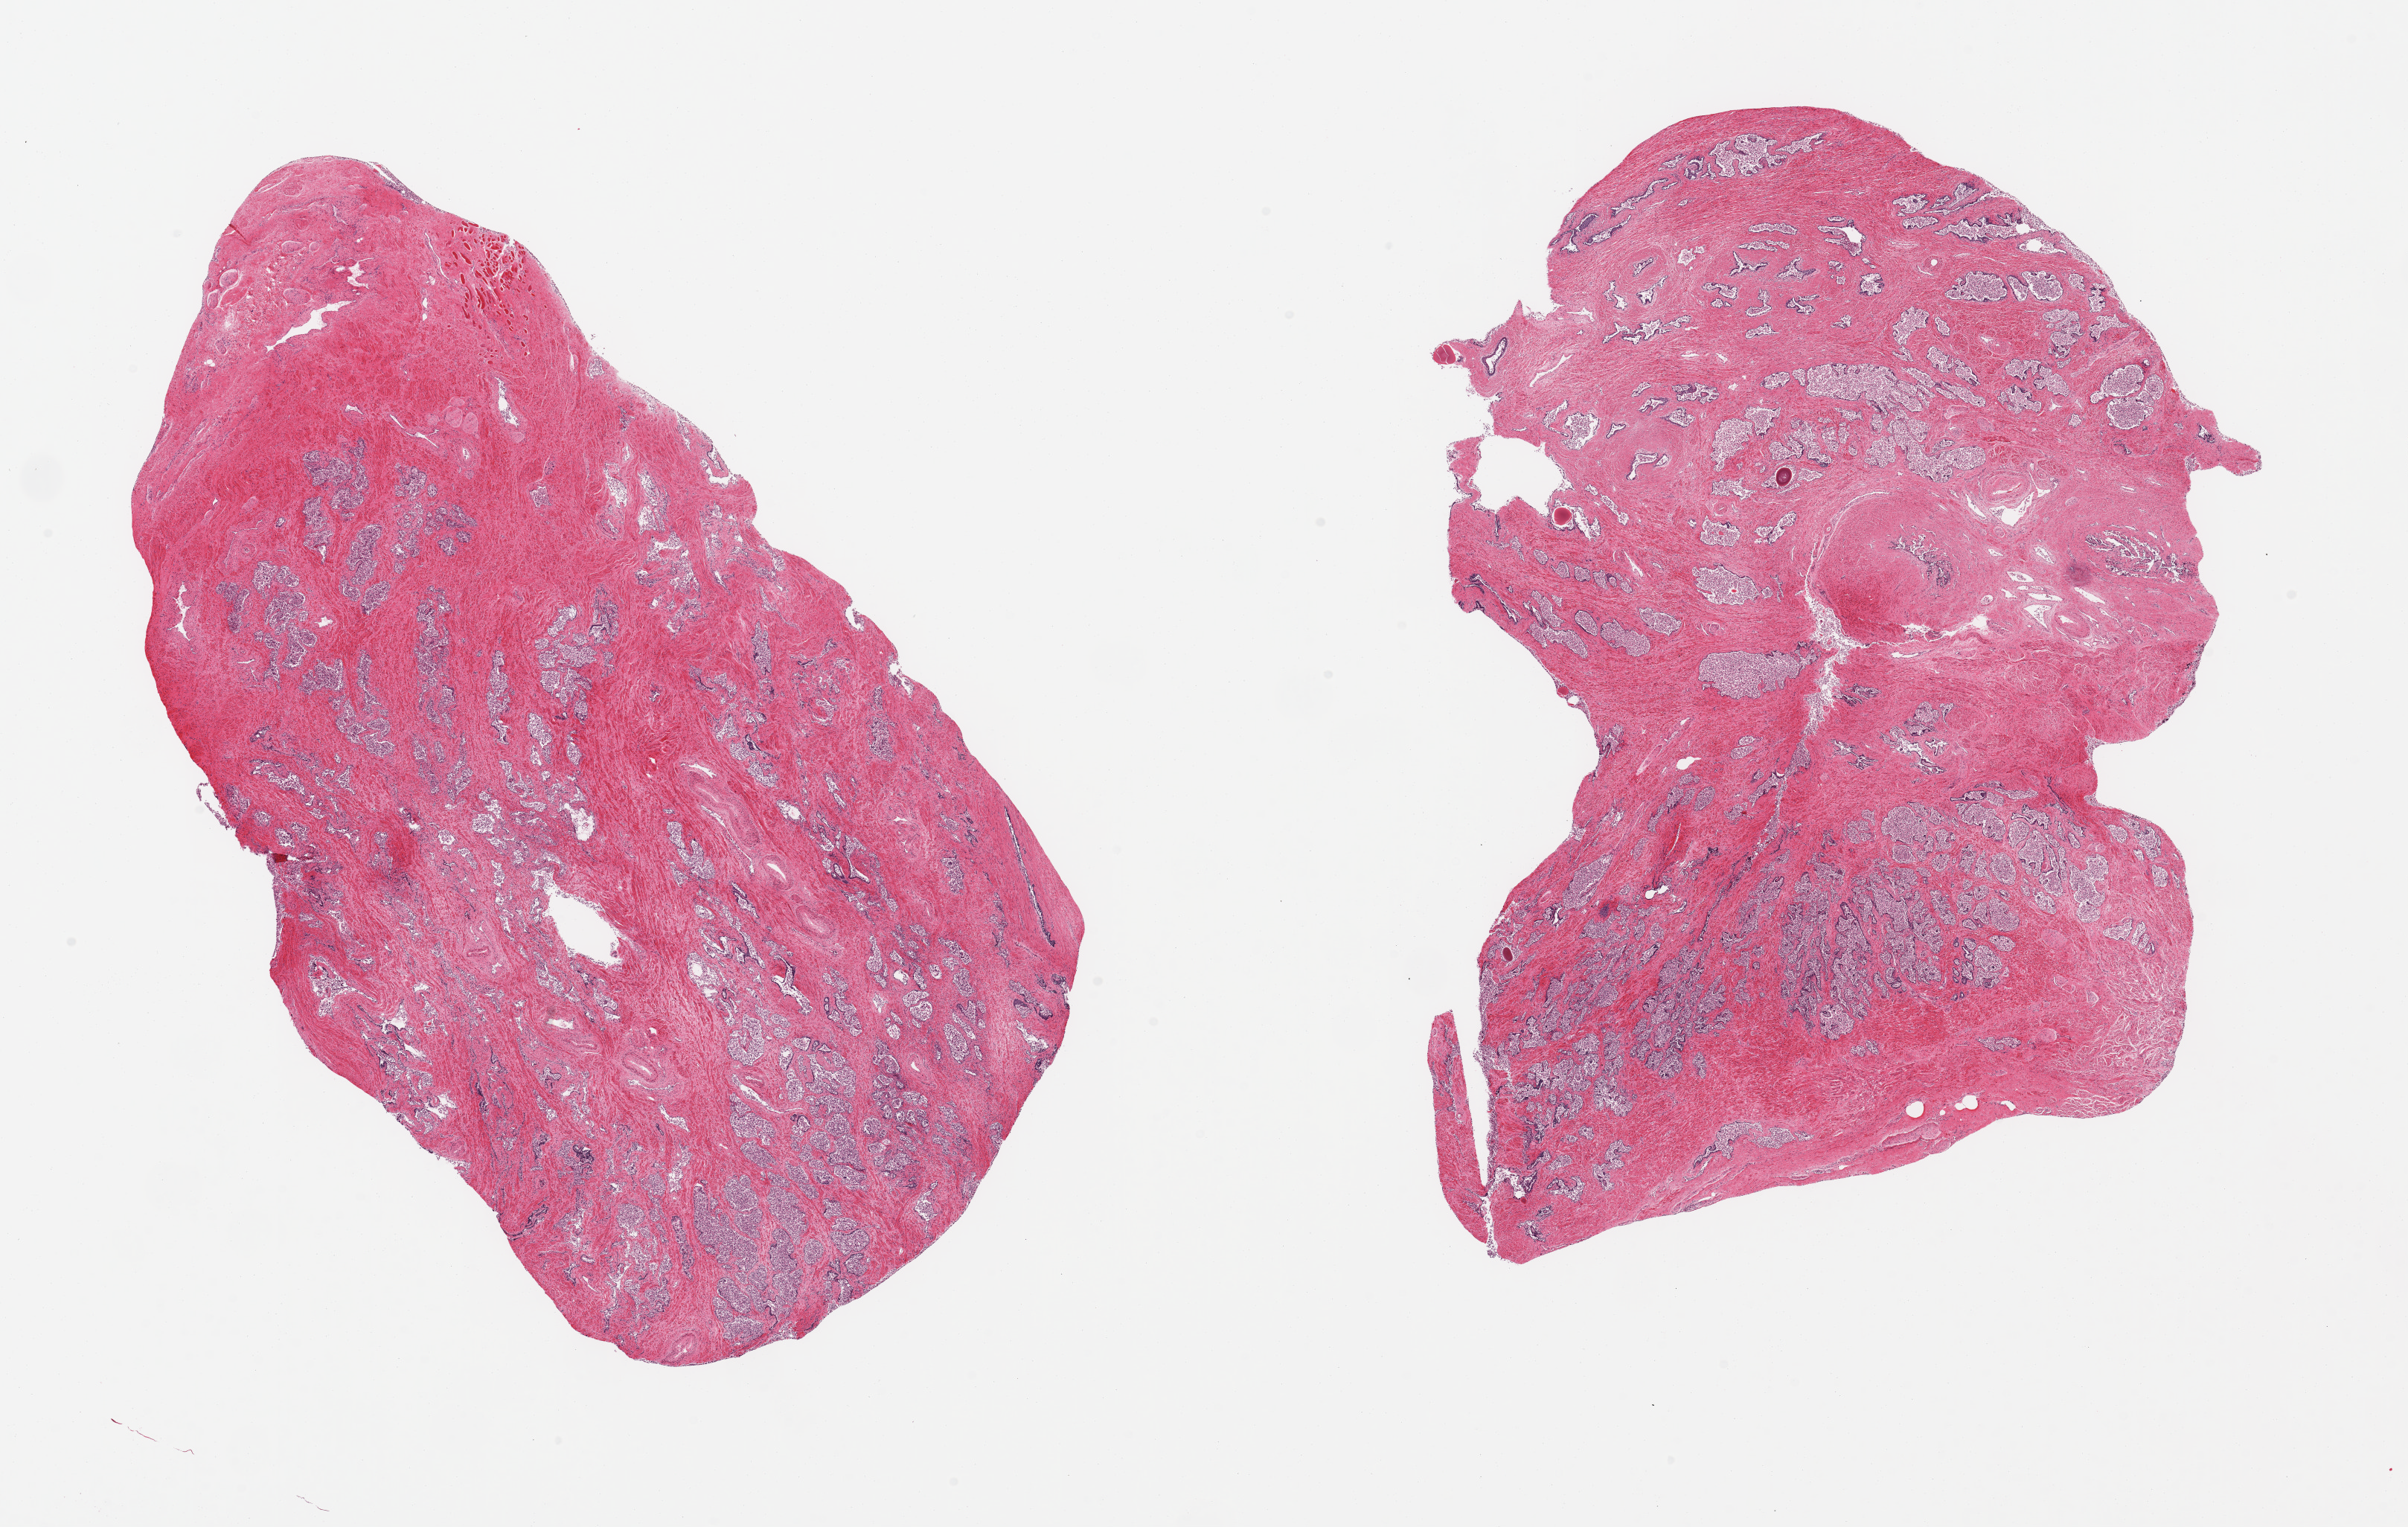
Hematoxylin and eosin (H&E) whole-slide image — a low-resolution overview of the entire scanned area, about 25.6 x 16.2 mm (from a 20x scan), PAXgene-fixed, paraffin-embedded tissue, target tissue: prostate, tissue donor sample.
Pathologist's review note for this sample: 2 pieces, glandular elements with advanced autolysis.